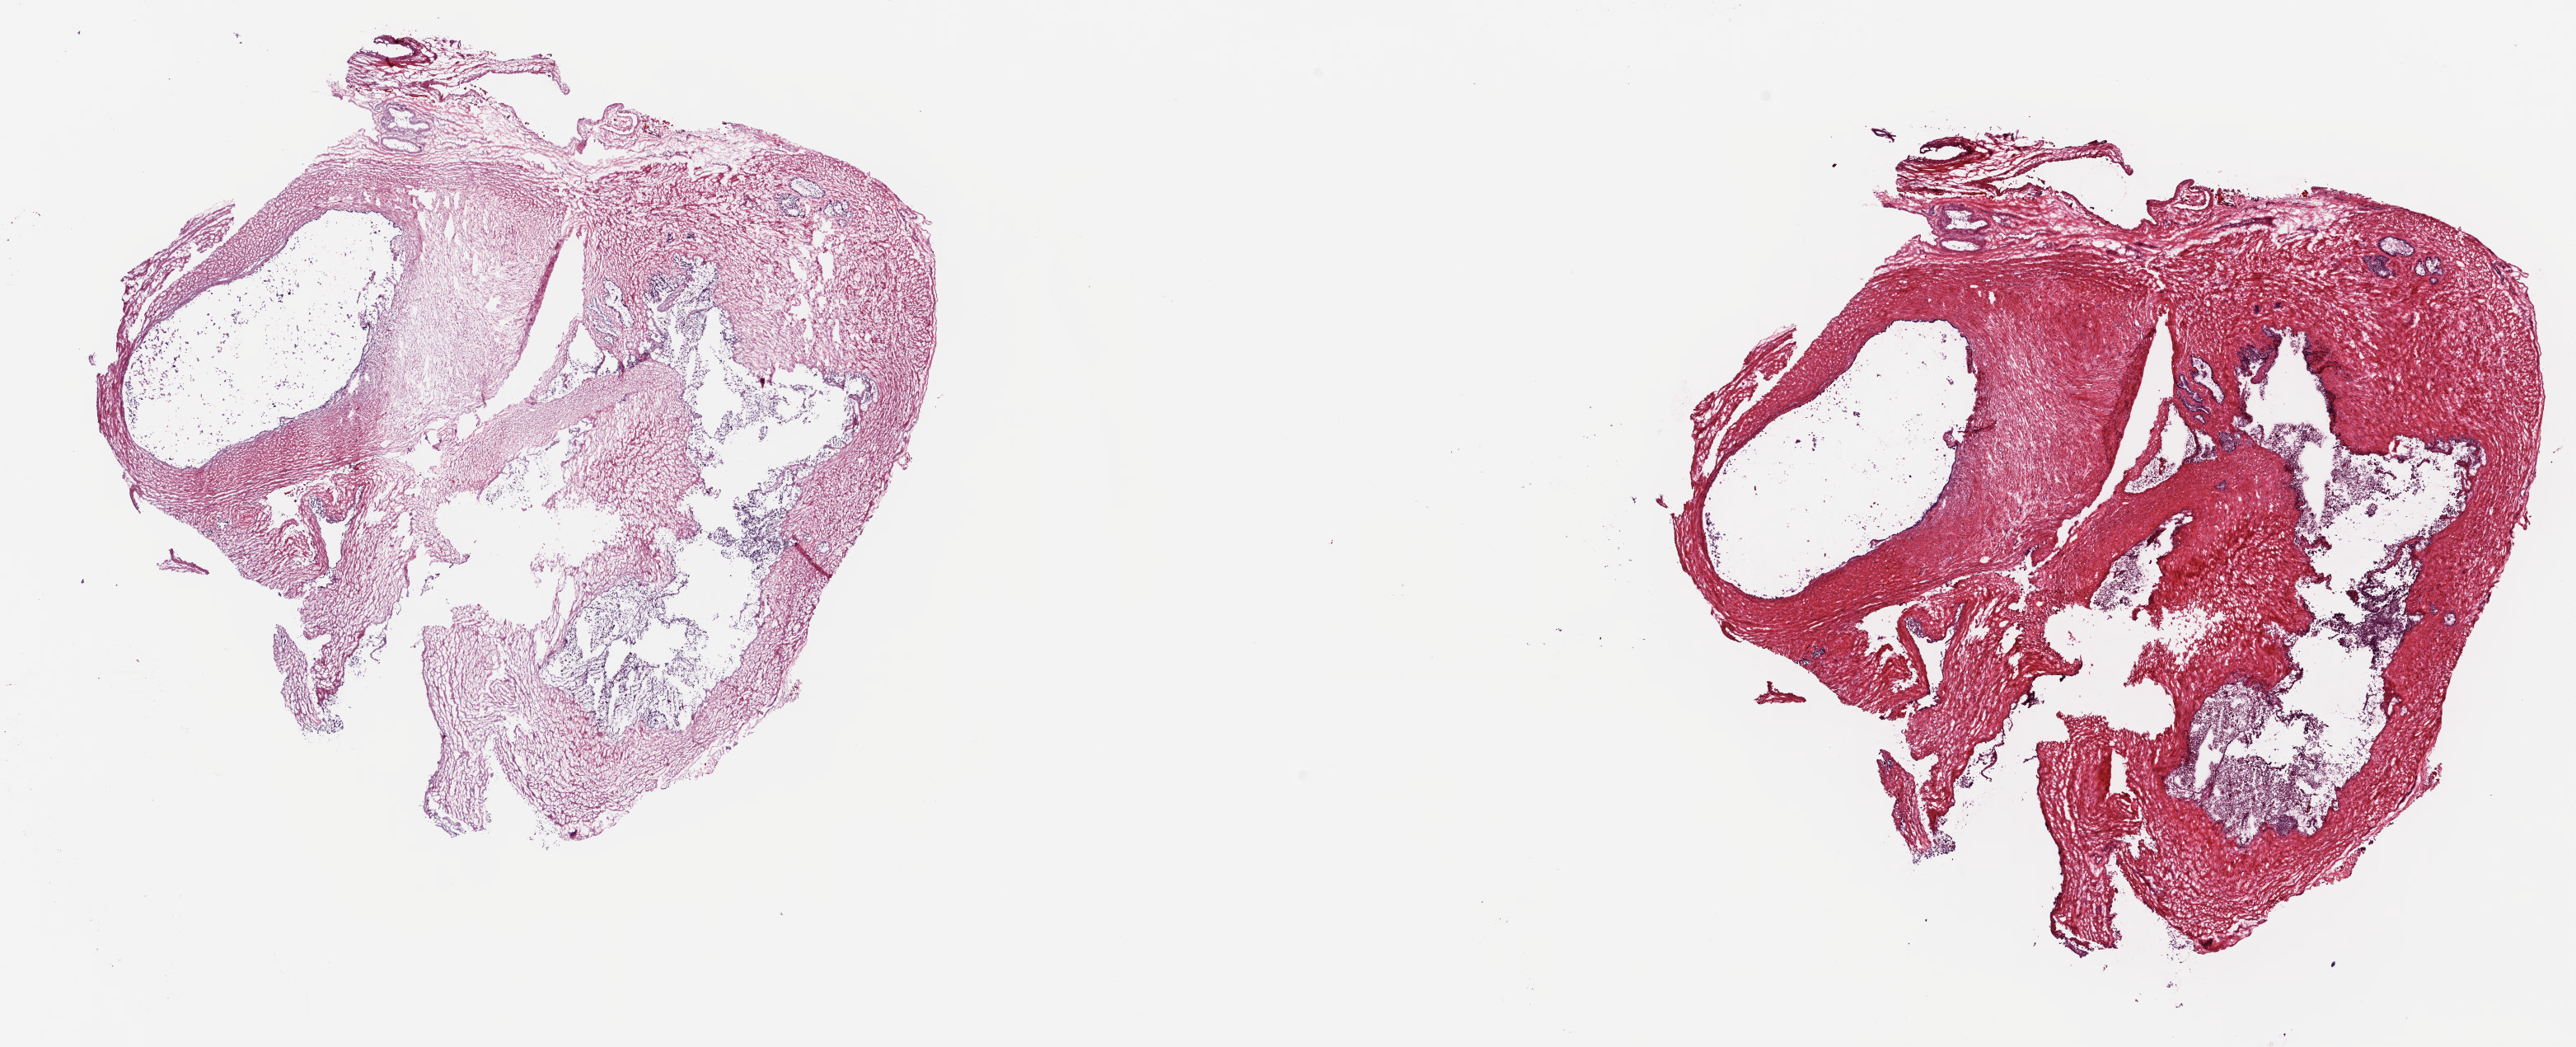
Whole-slide histology image, H&E-stained — a low-resolution overview of the entire scanned area, about 24.8 x 10.1 mm; frozen section; prostate, solid tissue normal (non-tumour tissue) sample. Patient: male, age at initial diagnosis 63 years. Pathologist review of this section (percent, as recorded): tumour cells 0%, tumour nuclei 0%, normal cells 100%, stromal cells 0%, necrosis 0%. Inflammatory infiltration, as recorded: lymphocyte infiltration 0%, monocyte infiltration 0%, neutrophil infiltration 0%.
This section: solid tissue normal sample (biorepository sample class). Patient diagnosis: Adenocarcinoma, NOS (prostate gland).